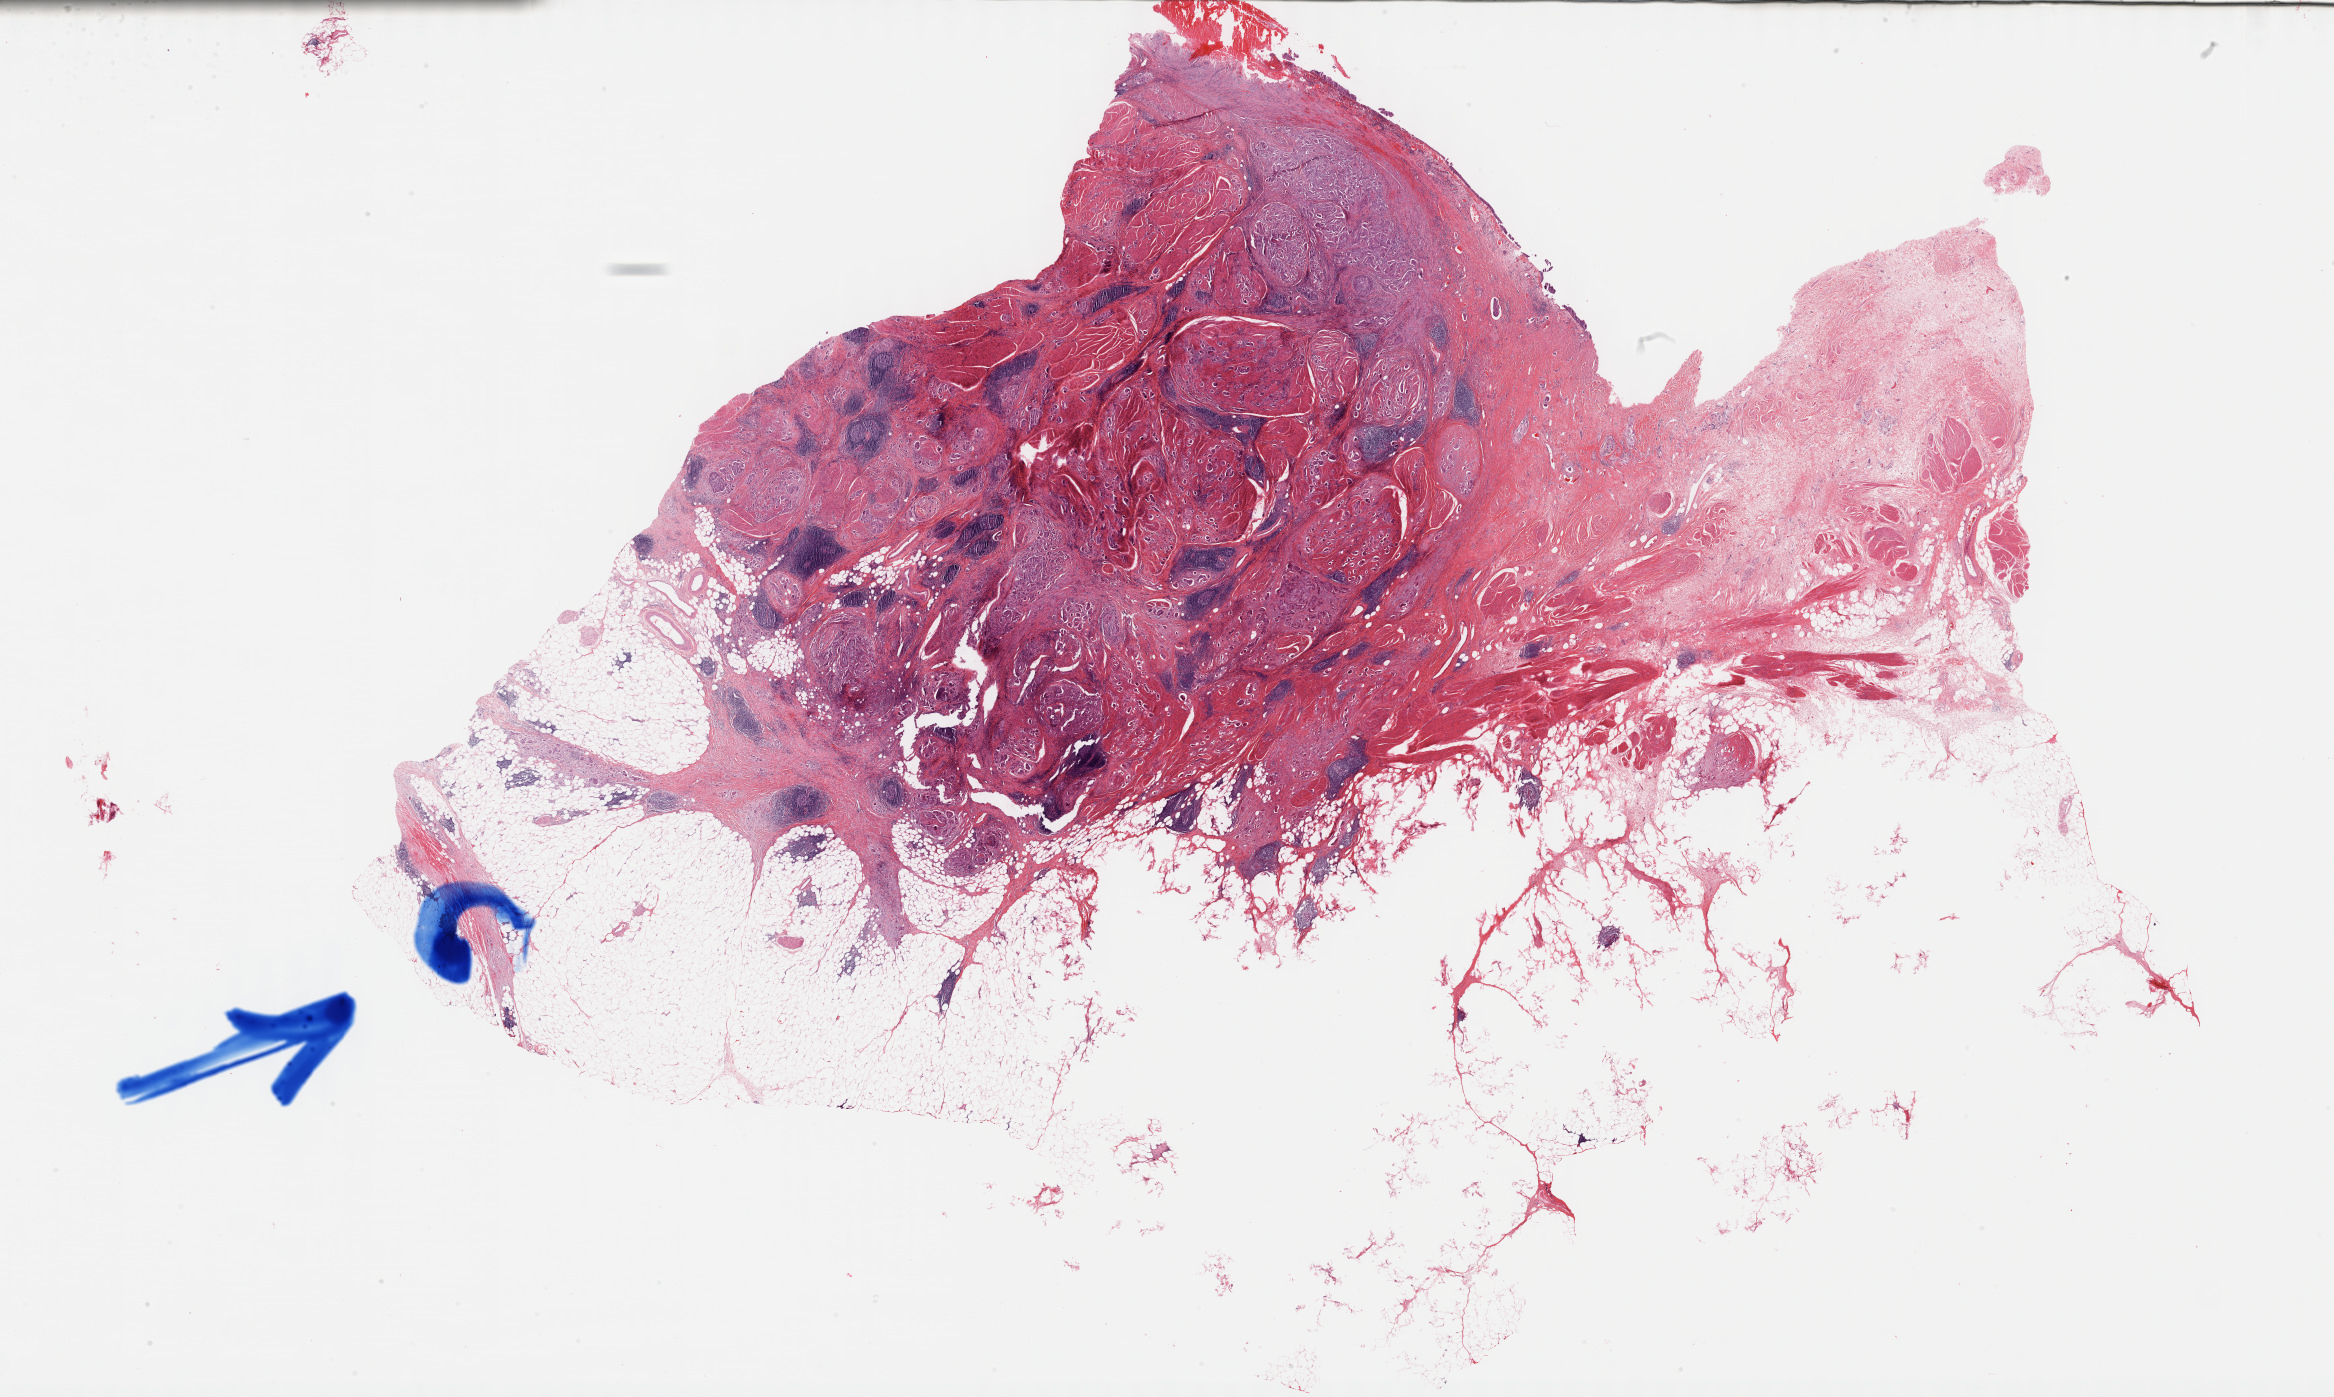
Whole-slide histology image, H&E, low-resolution overview of the scanned area, about 37.8 x 22.6 mm (slide scanned at 40x), FFPE section, sample: primary tumour, bladder. Patient: male, age at initial diagnosis 77 years. Histologic grade: high grade.
AJCC pathologic stage: IV (7th edition). Histologic diagnosis: Papillary transitional cell carcinoma.